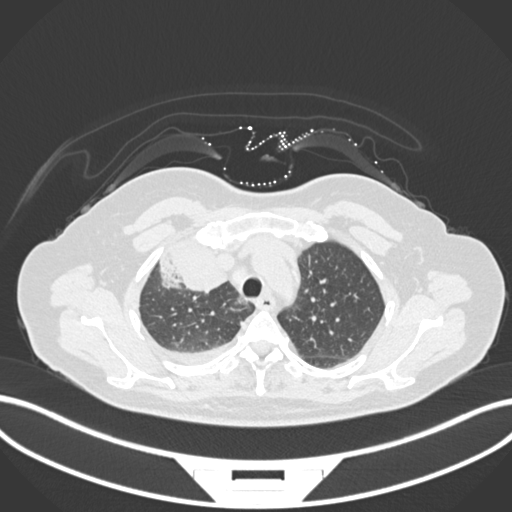
Chest CT, one axial slice; slice 128 of 172 in the series (ordered by position); reconstruction kernel B30f; 120 kVp; lung window (W 1500 / L -600 HU); 512 × 512 image matrix. Female patient, age 52 years. Case-level facts recorded for this patient, not image findings: clinical TNM (as recorded): T3 N1 M1.
Structures marked on this image (bounding box drawn by a radiologist):
- lung tumour (recorded histology: adenocarcinoma): bounding box [x1, y1, x2, y2] px = [155, 248, 227, 293]